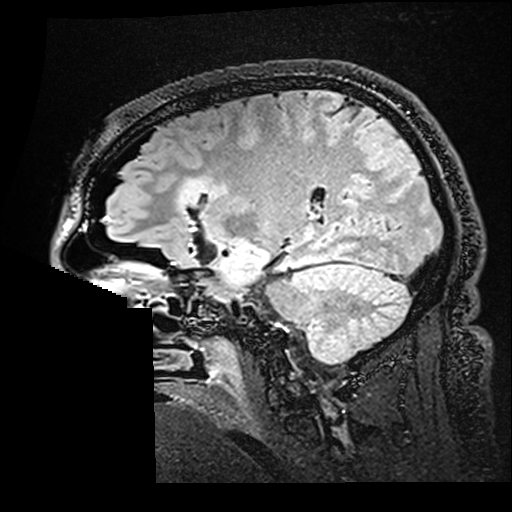
Brain MRI from a brain-tumour surgery series, one sagittal slice. Position 111 of 176 along the scan axis. T2 FLAIR. 512 × 512 image matrix, field of view 250 × 250 mm. Case-level facts recorded for this patient, not image findings: histopathology: Astrocytoma; WHO grade: 2; IDH mutation: yes; tumour location: Right Insular.
Annotated regions visible in this slice (outlined manually by an expert reader):
- residual tumour: bounding box (x1, y1, x2, y2) in pixels: (179, 178, 228, 208)